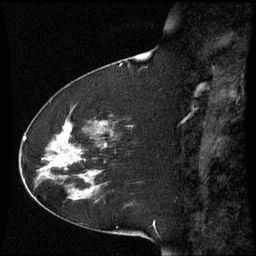
Breast MRI (dynamic contrast-enhanced), one sagittal slice. Slice 20 of 60 in the series (ordered by position). Dynamic contrast-enhanced series, image 2 of 3 at this slice position (ordered by acquisition). 1.5 T. TE 4.2 ms, TR 8.9 ms. 256 × 256 image matrix, field of view 210 × 210 mm. Female patient, age 51 years. From the clinical record (not read from this slice): setting: breast cancer imaged before/during neoadjuvant chemotherapy; receptor status: HR-positive, HER2-negative.
Outlined on this slice (semi-automatic segmentation, software-assisted and operator-edited):
- analysis volume of interest (the breast-tissue region the enhancement analysis was run in; not a lesion): box from (x=50, y=117) to (x=114, y=187) px
- tumour enhancement mask (voxels above the 70 % enhancement threshold inside the analysis volume of interest): (x=58, y=123)–(x=88, y=181)